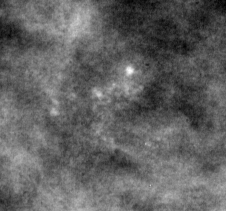
Cropped region of a digitized screen-film mammogram centred on a radiologist-marked abnormality; right breast; CC view; BI-RADS breast density category 3 (scale 1–4).
Calcifications, morphology pleomorphic, distribution clustered; BI-RADS assessment category 4; pathology result (as recorded, not read from the image): malignant.